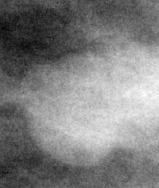
Region of interest cut from a scanned film mammogram (one marked finding), right breast, CC view.
Mass, shape lobulated, margins circumscribed; BI-RADS assessment category 3; benign; no additional work-up was recommended (benign without callback).